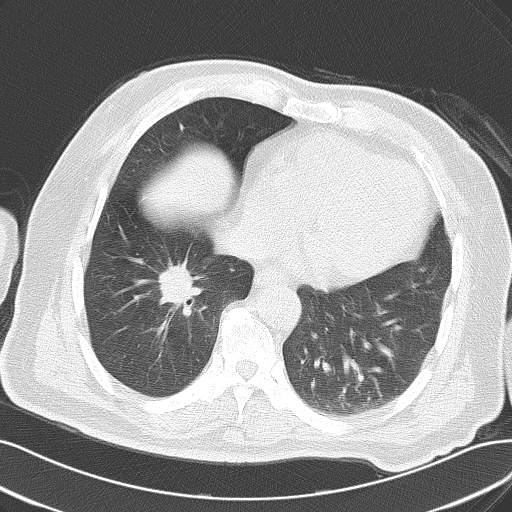
Chest CT, one axial slice; slice 26 of 61 in the series (ordered by position); reconstruction kernel B70f; 120 kVp; lung window (W 1500 / L -600 HU); 512 × 512 image matrix, field of view 363 × 363 mm. Patient: male, 69 years. From the clinical record (not read from this slice): clinical TNM (as recorded): T1c N0 M0.
Outlined on this slice (bounding box drawn by a radiologist):
- lung tumour (recorded histology: adenocarcinoma): box from (x=155, y=260) to (x=196, y=307) px